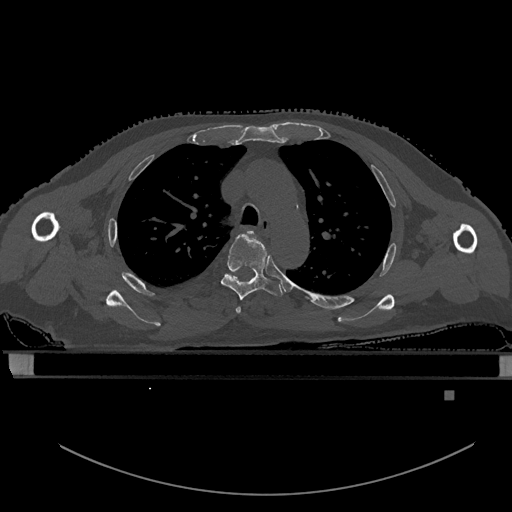
CT including the spine, one axial slice; slice 408 of 969 in the series (ordered by position); bone window (W 1800 / L 400 HU); 0.5 mm slice thickness; 512 × 512 image matrix, field of view 456 × 456 mm. Patient: male, 82 years. From the clinical record (not read from this slice): primary cancer: prostate.
Structures marked on this image (semi-automatic segmentation, software-assisted and operator-edited):
- T3 vertebra: box from (x=235, y=230) to (x=253, y=314) px
- T4 vertebra: (x=221, y=234)–(x=283, y=300)